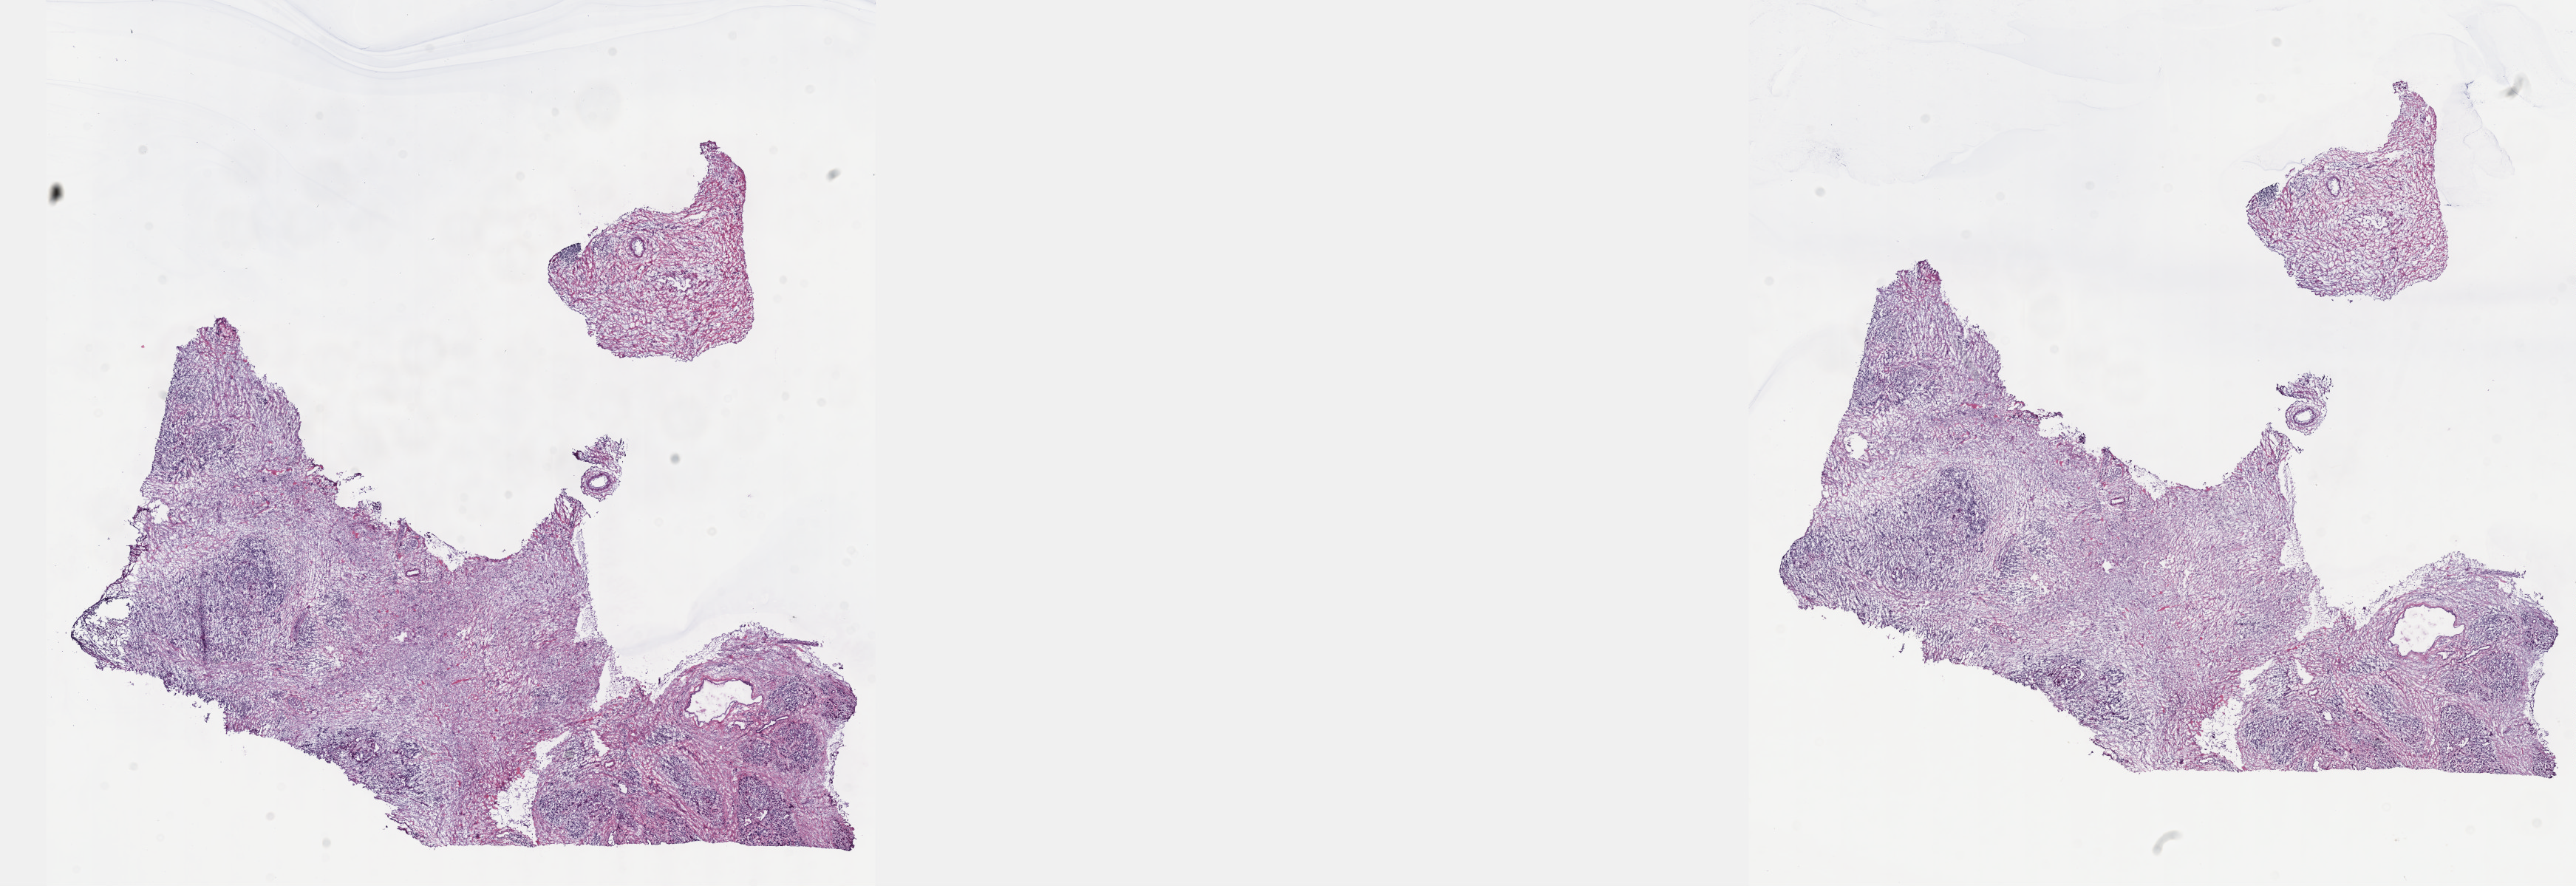
Digitized H&E tissue section (whole slide) — whole scanned area (about 28.2 x 9.7 mm) shown as a low-resolution overview; frozen section from the top of the tissue portion; pancreas, primary tumour sample. Male, age 49 years at initial diagnosis. Histologic grade: G2 (moderately differentiated). Composition of this section per pathologist review: tumour cells 100%, tumour nuclei 60%, normal cells 0%, stromal cells 0%, necrosis 0%. Inflammatory infiltration, as recorded: lymphocyte infiltration 5%, monocyte infiltration 0%, neutrophil infiltration 0%.
* lymph nodes positive (case pathology): 3 of 15 examined
* AJCC pathologic stage: IIB (7th edition)
* diagnosis: Infiltrating duct carcinoma, NOS